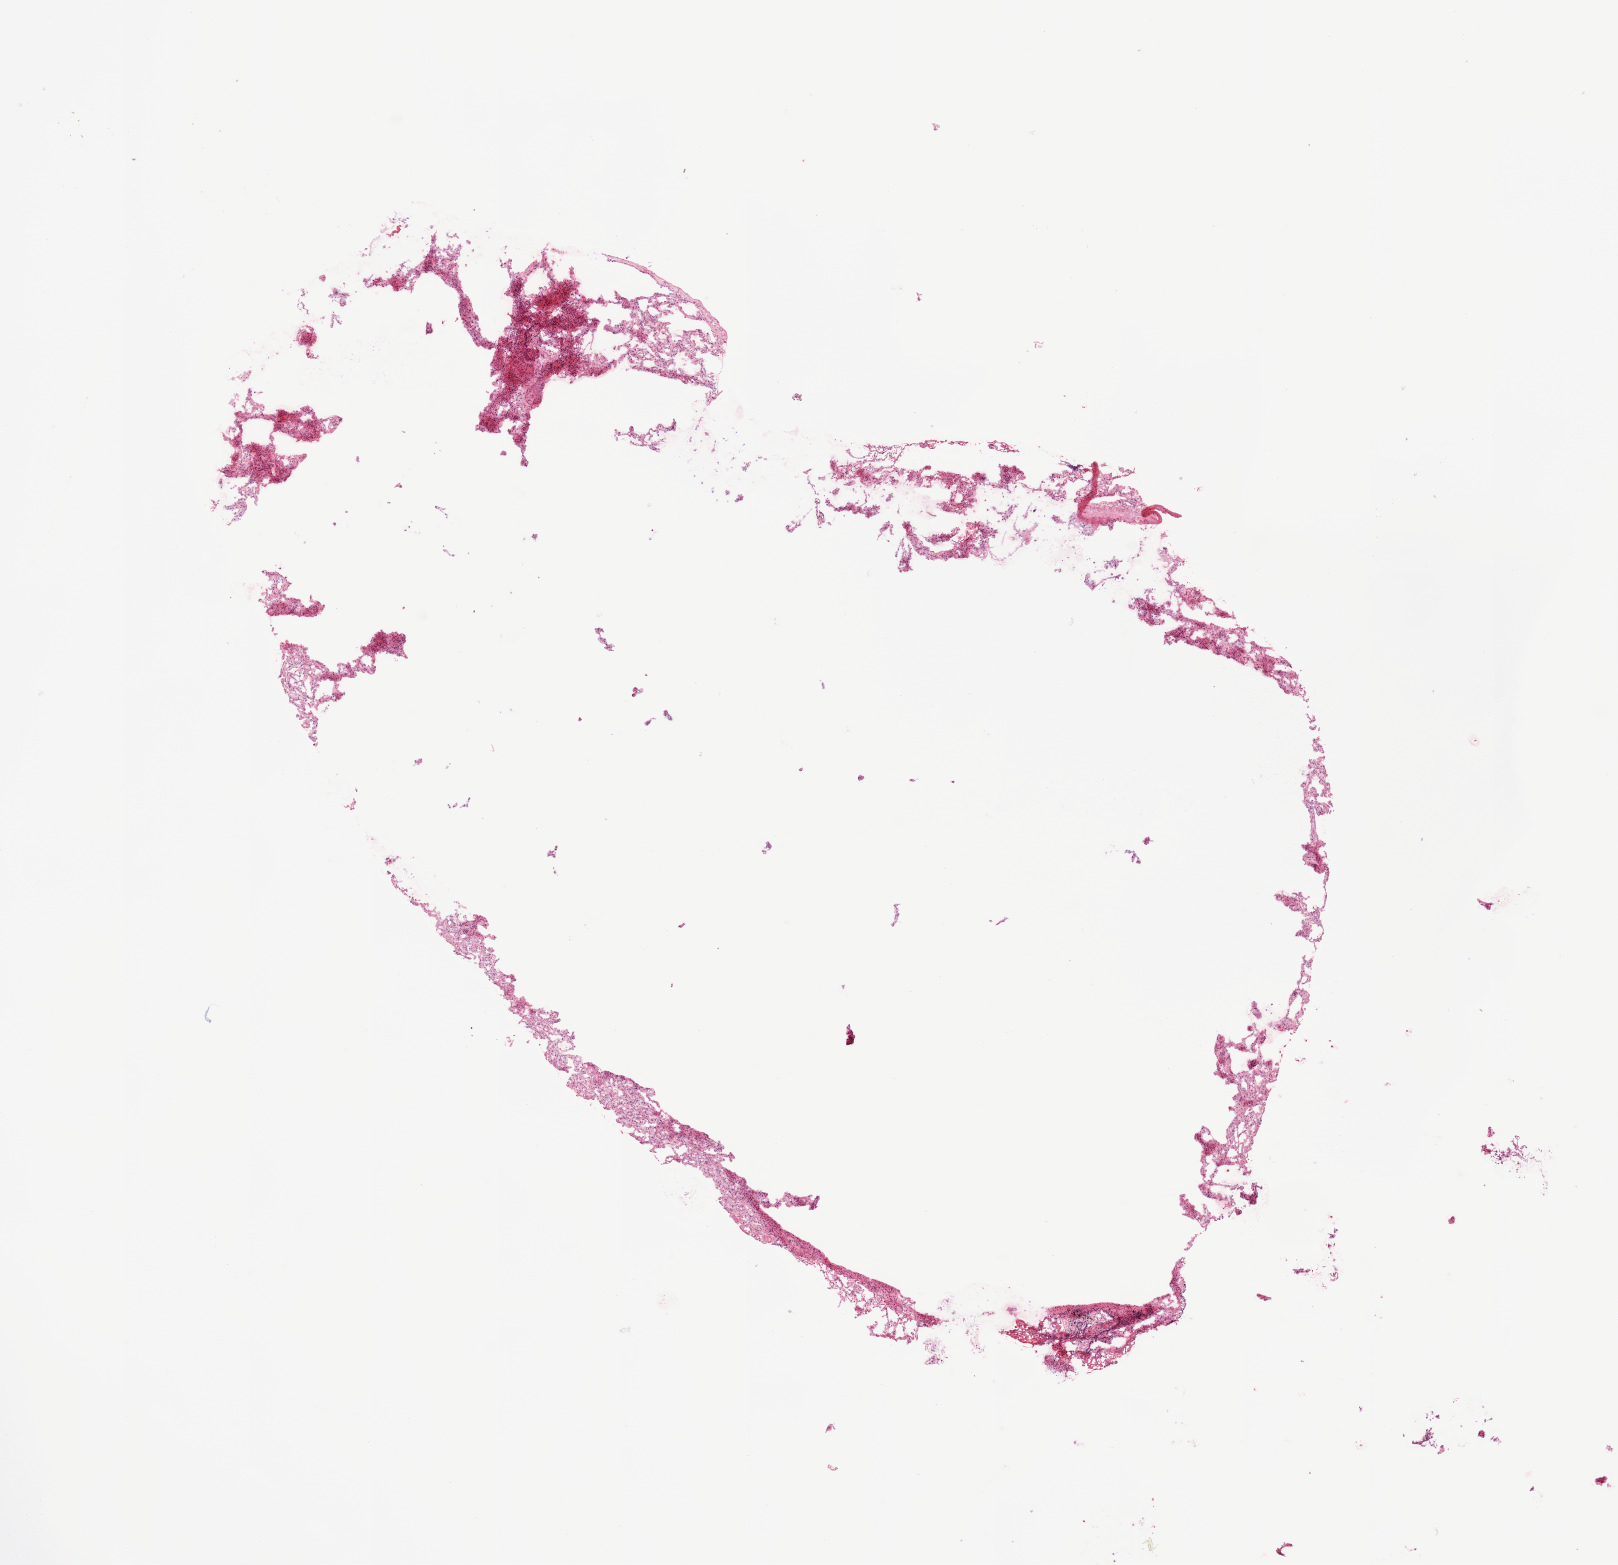
Digitized H&E-stained tissue section (whole slide) — a low-resolution overview of the entire scanned area, about 12.8 x 12.4 mm; lung, normal (non-tumour) tissue. Female, 75 y/o.
* this section: normal (non-tumour) tissue from the same patient
* patient diagnosis (cohort enrolment): squamous cell carcinoma (lung)